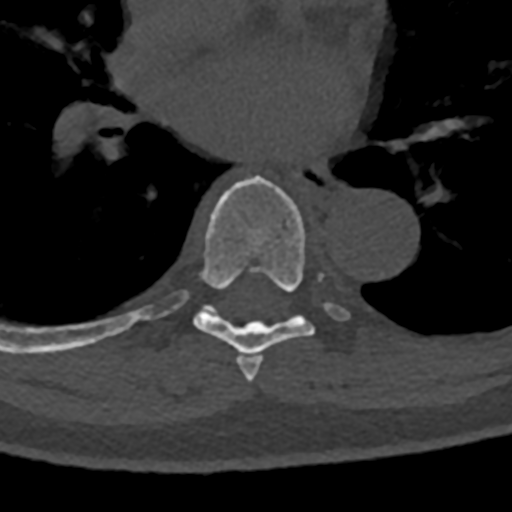
CT including the spine, one axial slice; position 758 of 797 along the scan axis; reconstruction kernel Br40s/3; 120 kVp; bone window (W 1800 / L 400 HU); 0.5 mm slice thickness; 512 × 512 image matrix, field of view 160 × 160 mm. Male patient, age 74 years. From the clinical record (not read from this slice): primary cancer: renal; vertebrae with lytic lesions (as recorded): T10, L1, L2, L3, L4, L5.
Outlined on this slice (semi-automatically segmented with operator editing):
- T6 vertebra: box from (x=244, y=357) to (x=263, y=382) px
- T7 vertebra: (x=70, y=176)–(x=351, y=373)
- T8 vertebra: (x=70, y=316)–(x=142, y=349)